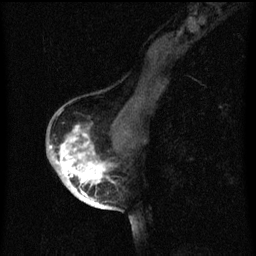
Breast MRI (dynamic contrast-enhanced), one sagittal slice; dynamic contrast-enhanced series, image 2 of 3 at this slice position (ordered by acquisition); 1.5 T; TE 4.2 ms, TR 8 ms; 256 × 256 image matrix, field of view 180 × 180 mm. Patient: female, 56 years.
Structures marked on this image (semi-automatic segmentation, software-assisted and operator-edited):
- analysis volume of interest (the breast-tissue region the enhancement analysis was run in; not a lesion): box from (x=54, y=126) to (x=120, y=199) px
- tumour enhancement mask (voxels above the 70 % enhancement threshold inside the analysis volume of interest): (x=56, y=126)–(x=111, y=199)